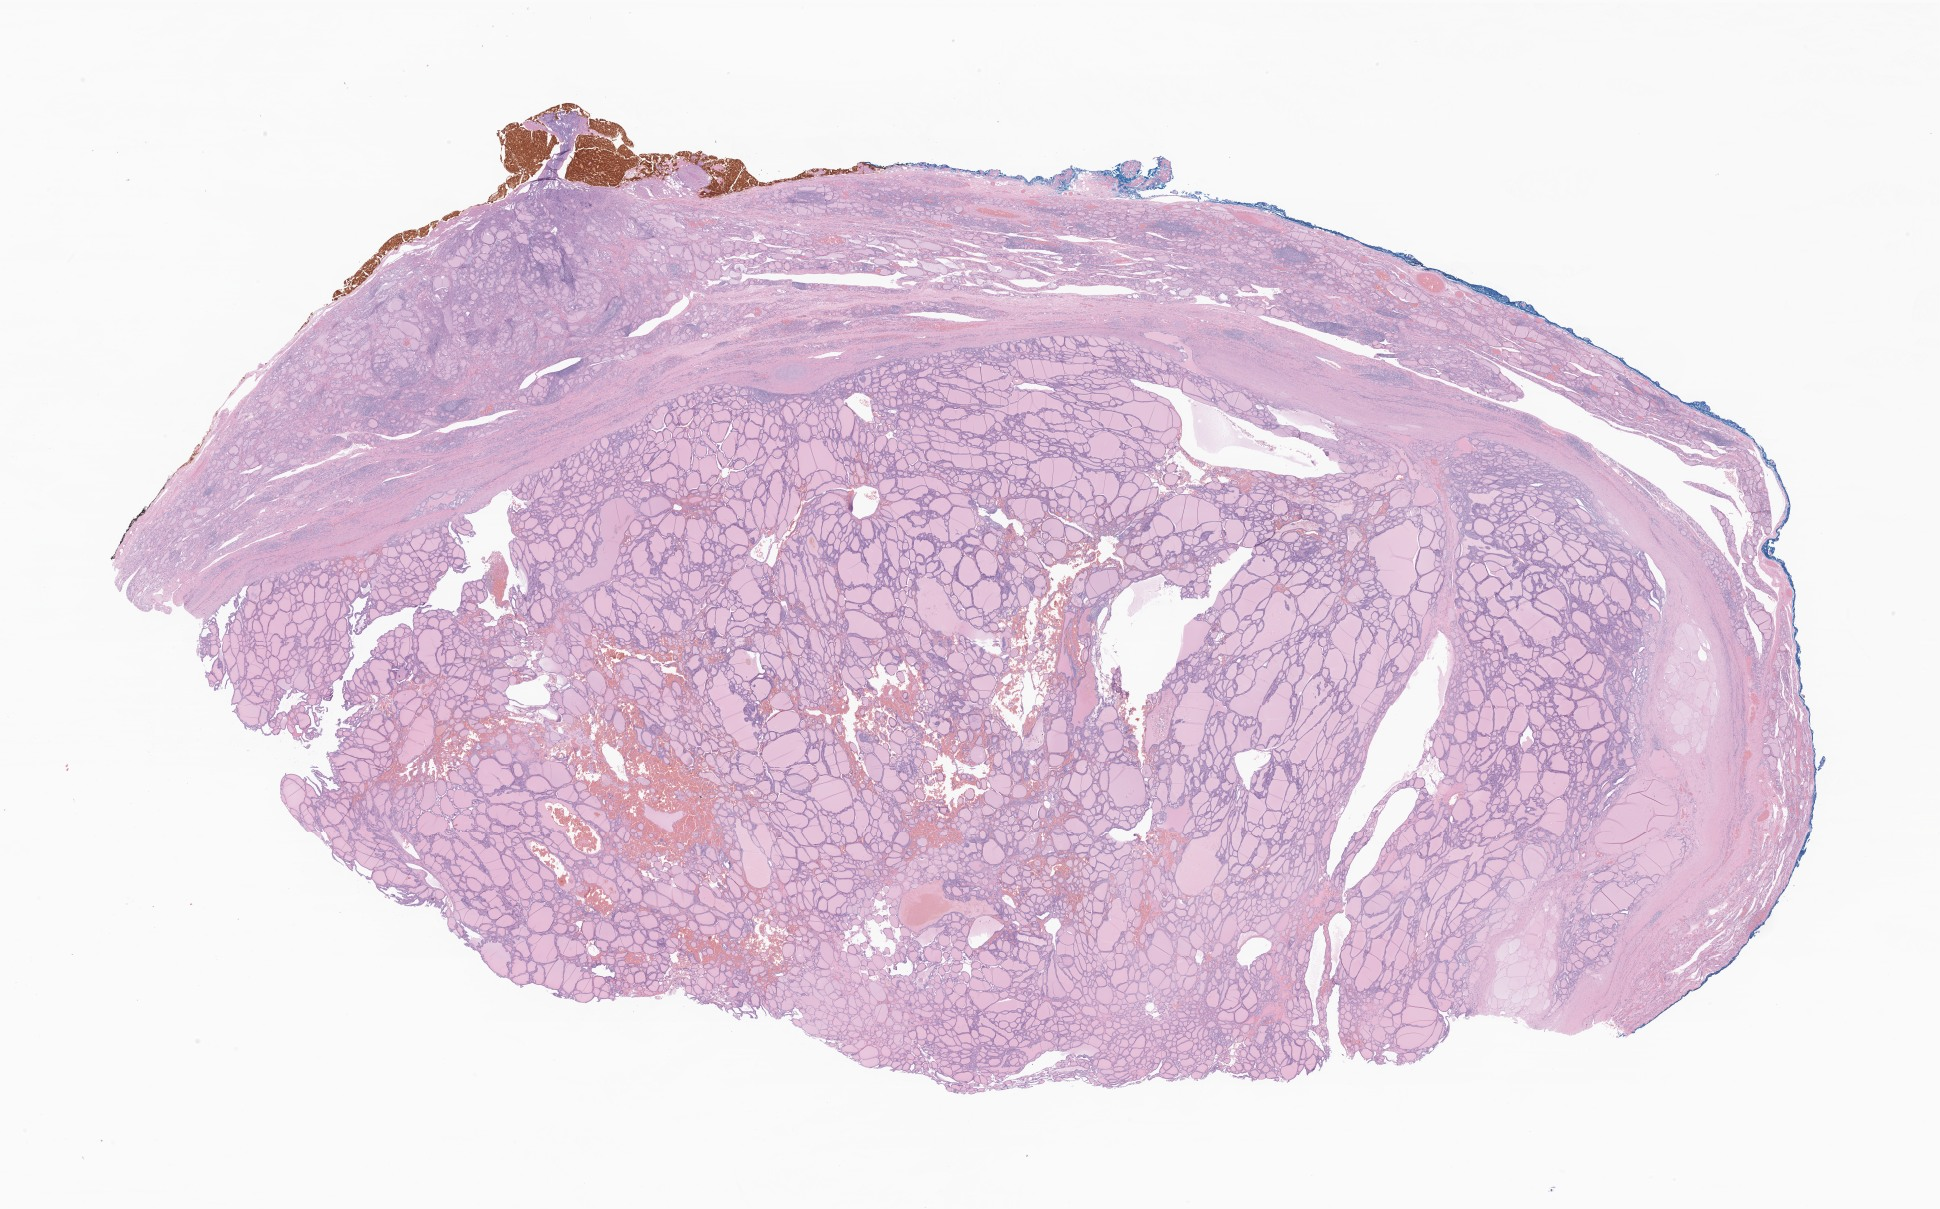
Haematoxylin and eosin whole-slide image of tumor tissue from the thyroid, a low-resolution overview of the entire scanned area, about 32.7 x 20.4 mm; formalin-fixed, paraffin-embedded (FFPE) tissue. Patient: male, age 183 months (15 years 3 months).
Recorded diagnosis: Papillary carcinoma, follicular variant.